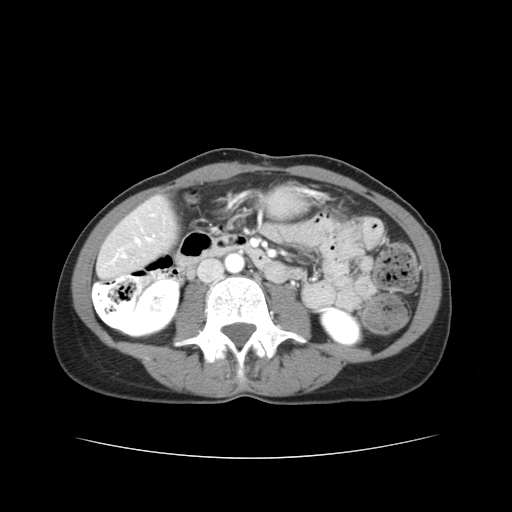
Contrast-enhanced abdominal CT, one axial slice; slice 8 of 38 in the series (ordered by position); 120 kVp; soft-tissue window (W 400 / L 40 HU); 512 × 512 image matrix, field of view 340 × 340 mm. Female patient, age 54 years. From the clinical record (not read from this slice): diagnosis: colorectal cancer liver metastases, imaged before liver resection; multiple liver metastases: yes; largest metastasis: 1.1 cm; chemotherapy before resection: yes.
Structures marked on this image (expert manual segmentation):
- hepatic veins: box from (x=136, y=239) to (x=140, y=243) px
- liver: (x=99, y=200)–(x=176, y=276)